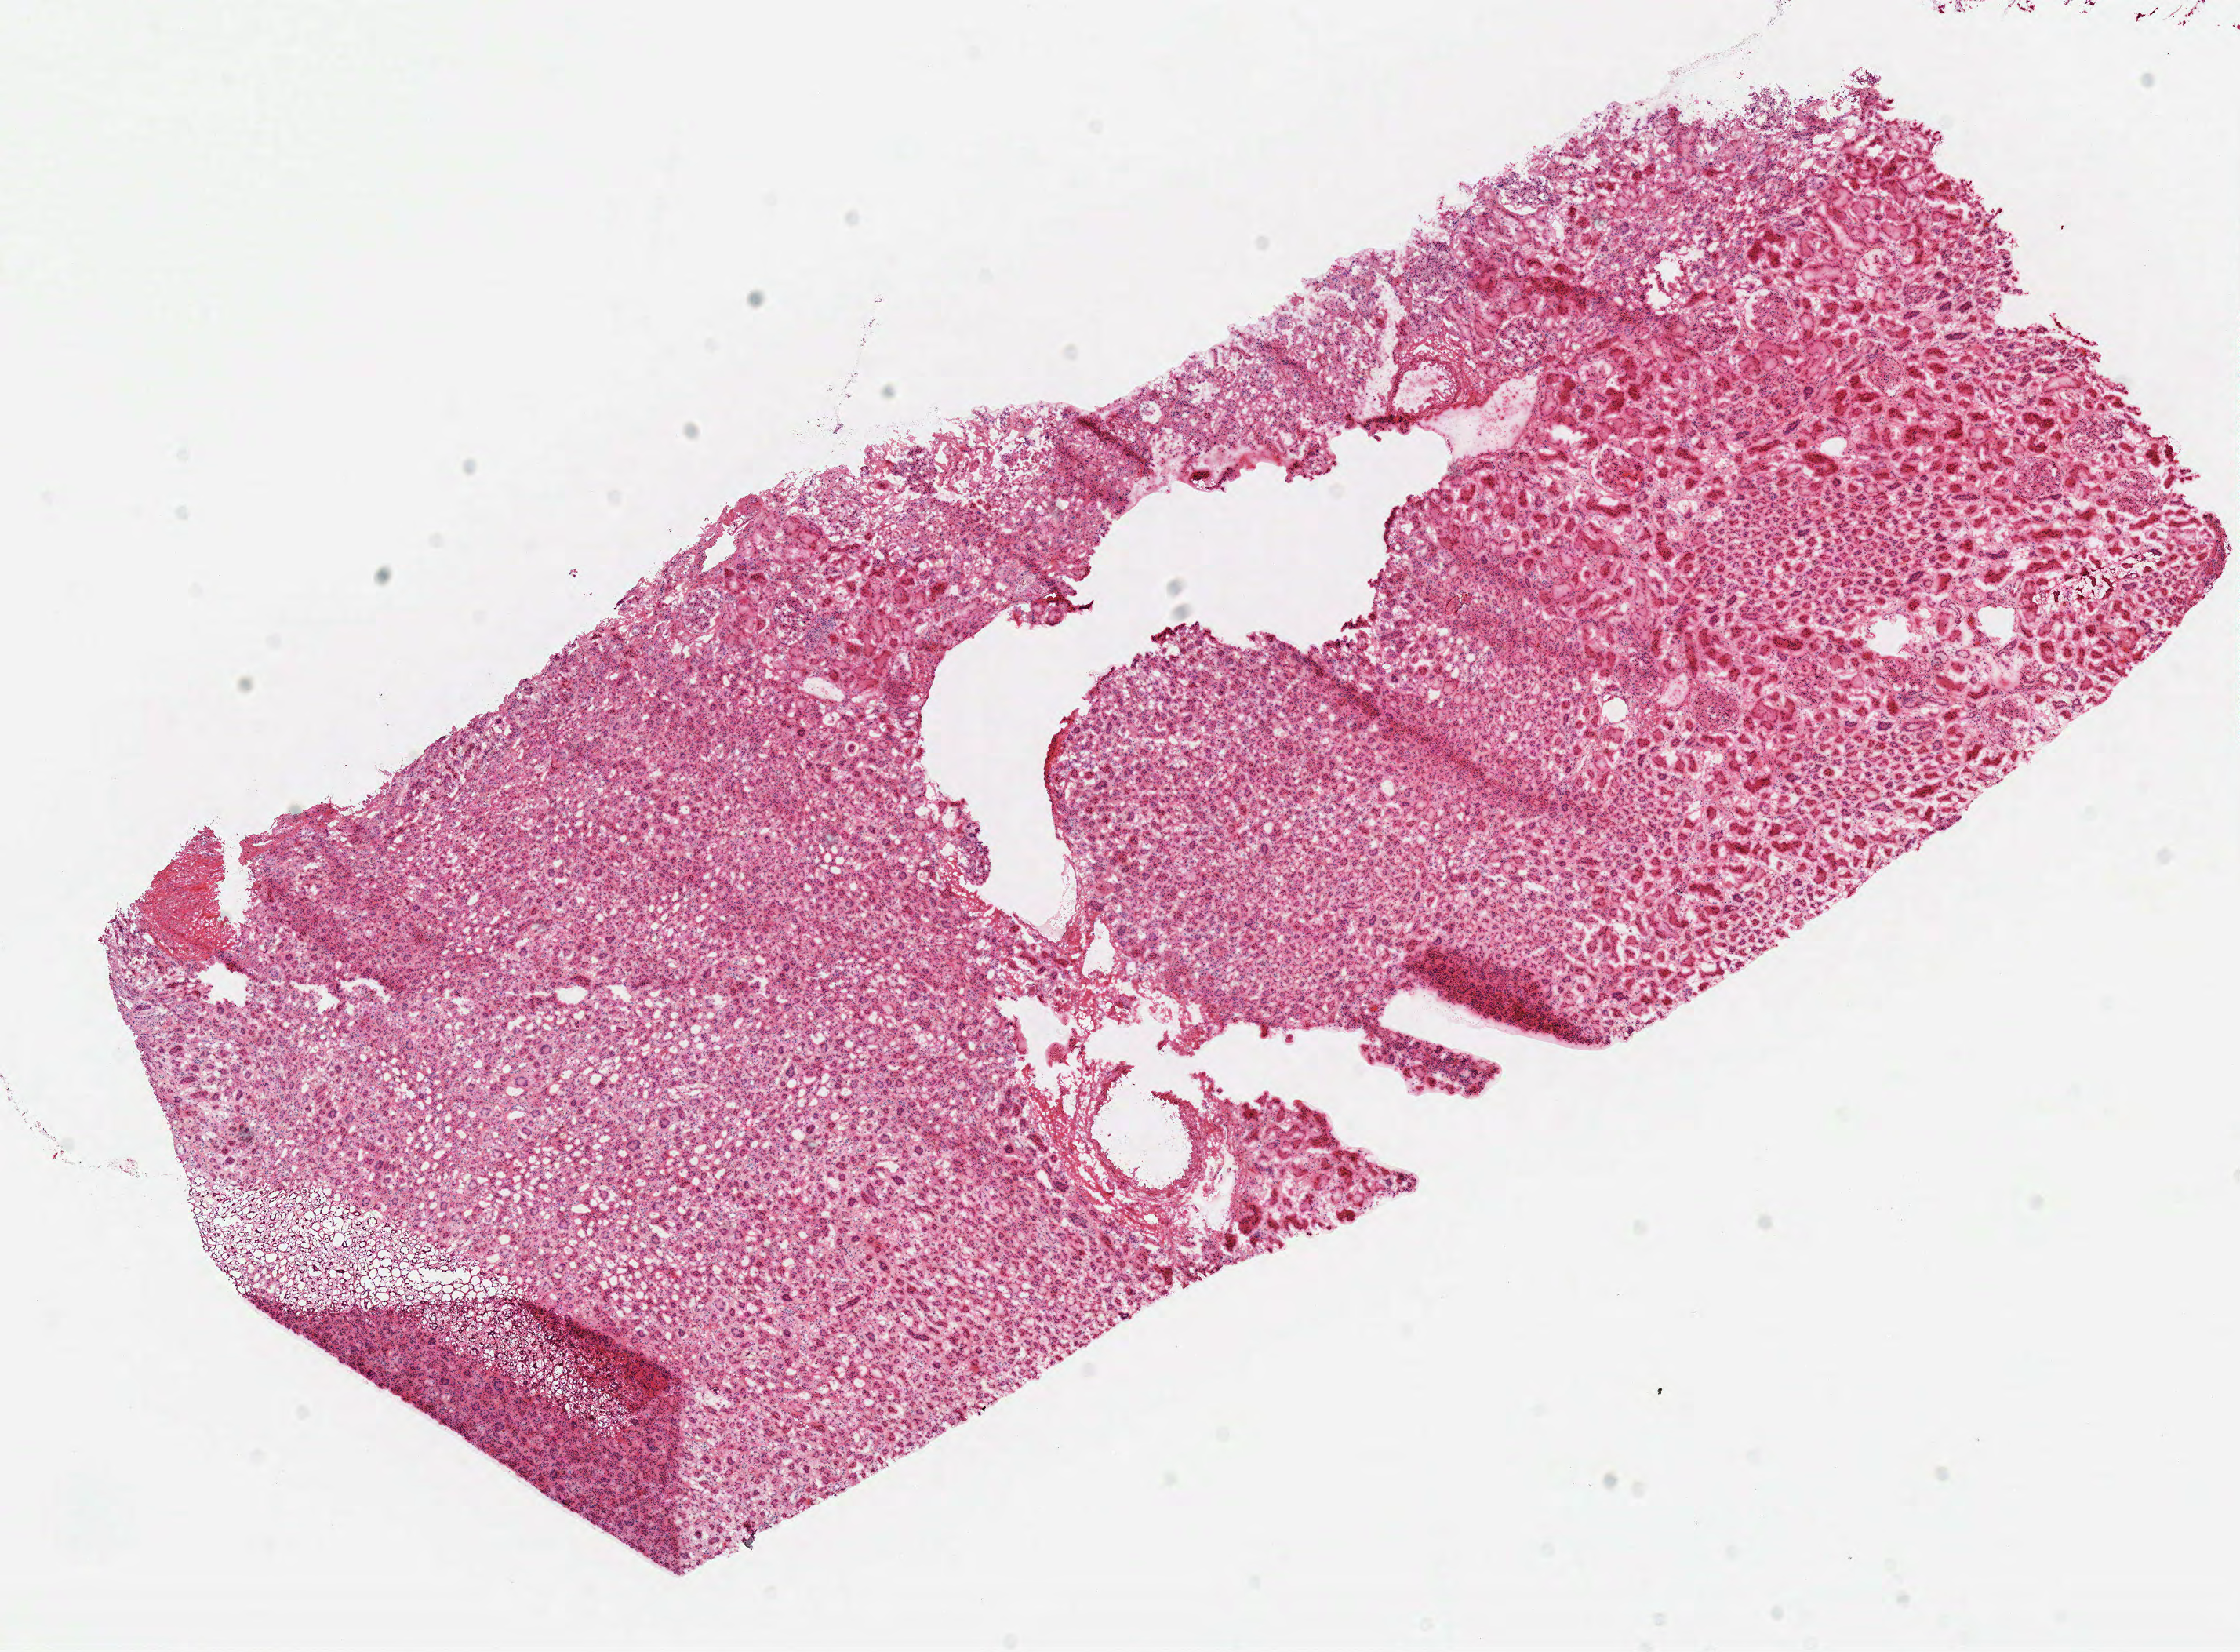
Whole-slide histology image, Hematoxylin and eosin (H&E) stained — a low-resolution overview of the entire scanned area, about 11.3 x 8.3 mm, frozen section from the top of the tissue portion, solid tissue normal (non-tumour tissue) sample from the kidney. Patient: male, age at initial diagnosis 31 years.
• this section: solid tissue normal (non-tumour) sample from the same patient
• patient diagnosis: Papillary adenocarcinoma, NOS